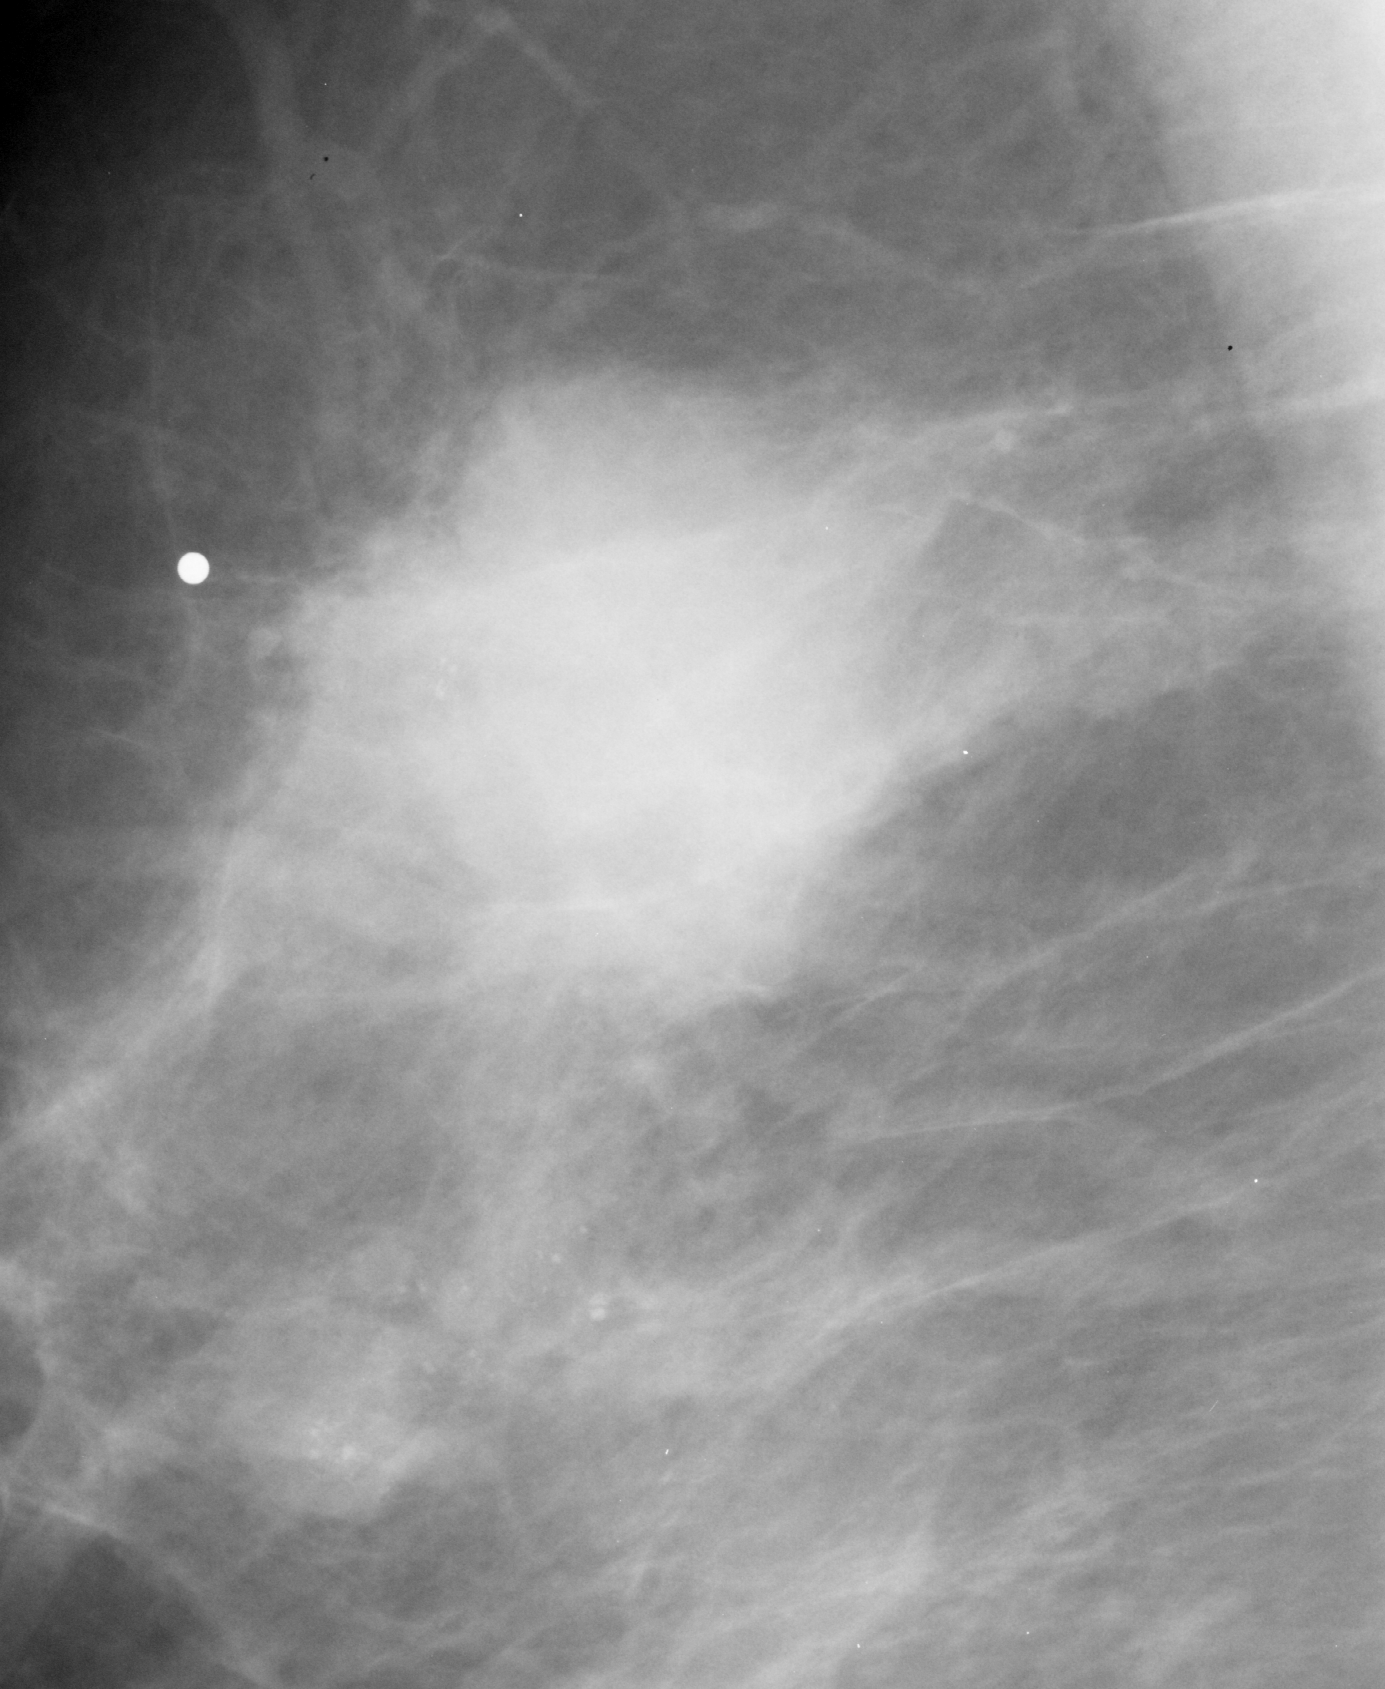
Cropped region of a digitized screen-film mammogram centred on a radiologist-marked abnormality; right breast; MLO view.
Calcifications, morphology amorphous, distribution clustered; BI-RADS assessment category 5; pathology result (as recorded, not read from the image): malignant.